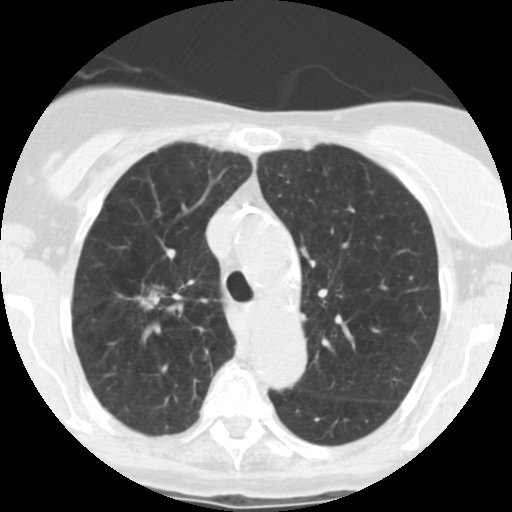
Low-dose screening chest CT, one axial slice. Slice 181 of 246 in the series (ordered by position). Reconstruction kernel STANDARD. Lung window (W 1500 / L -600 HU). 512 × 512 image matrix.
Structures marked on this image (outlined manually by an expert reader):
- lesion 1 (tumor, upper lobe of right lung): bounding box [x1, y1, x2, y2] px = [134, 290, 160, 309]